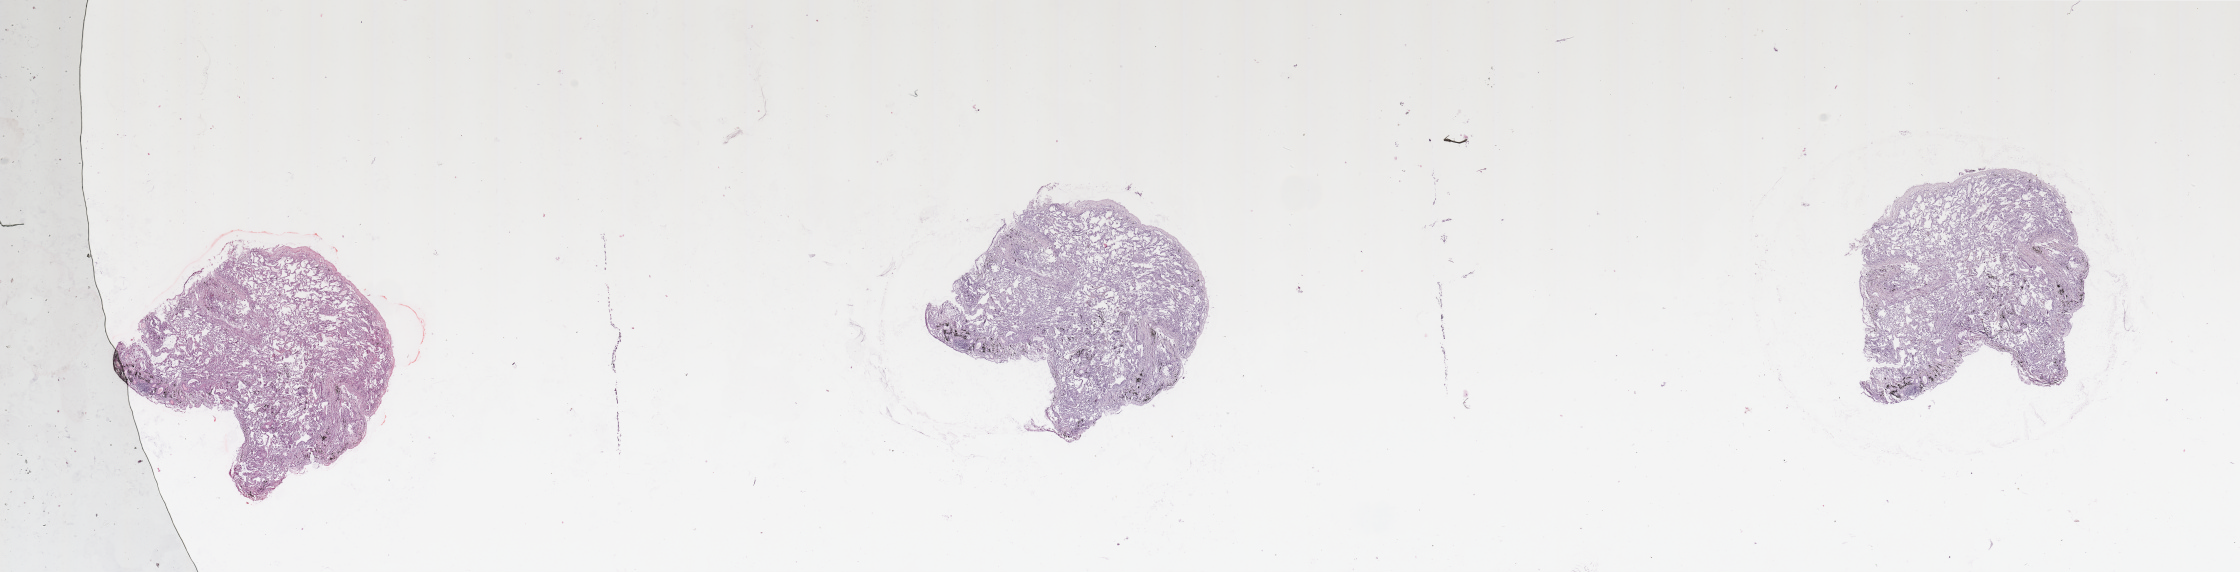
H&E-stained whole-slide image — a low-resolution overview of the entire scanned area, about 35.4 x 9.0 mm; normal (non-tumour) tissue sample, sampled site: lung. 76-year-old male patient.
This section: normal (non-tumour) tissue from the same patient. Patient diagnosis: Adenocarcinoma, NOS.